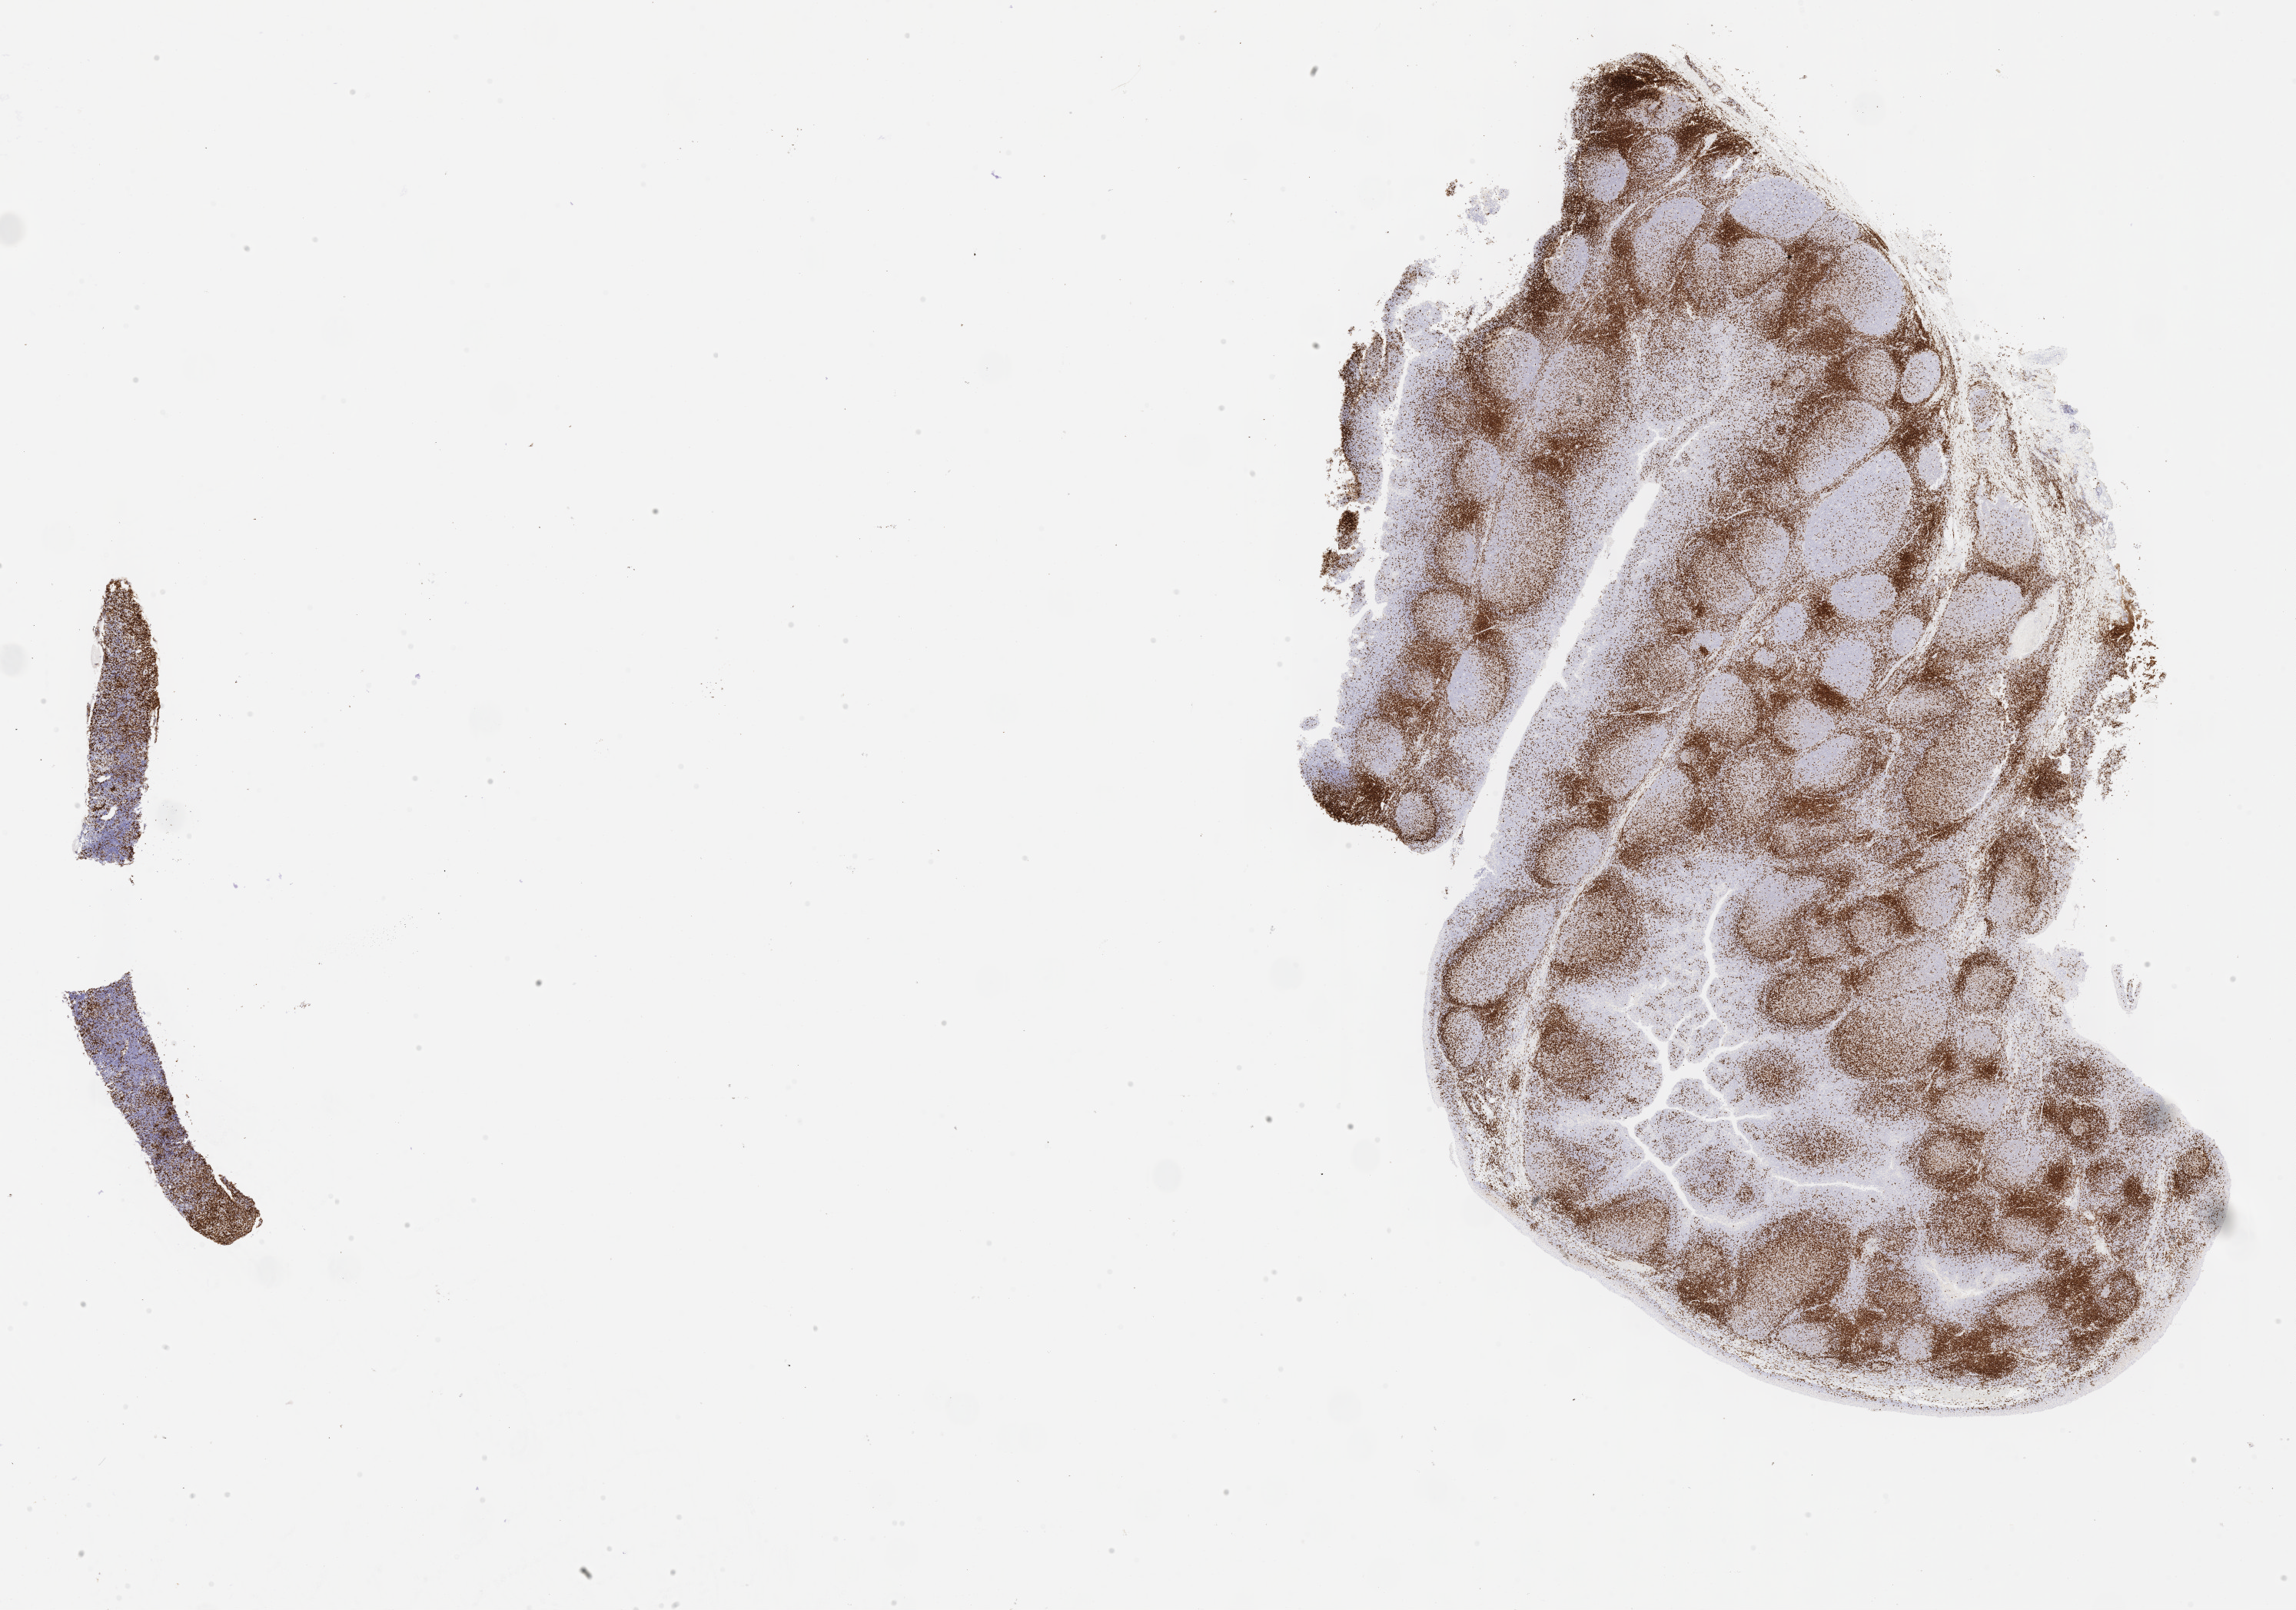
Immunohistochemistry (IHC) whole-slide image stained for CD3, a low-resolution overview of the entire scanned area, about 24.2 x 16.9 mm. Male patient.
Specimen: tumor tissue.